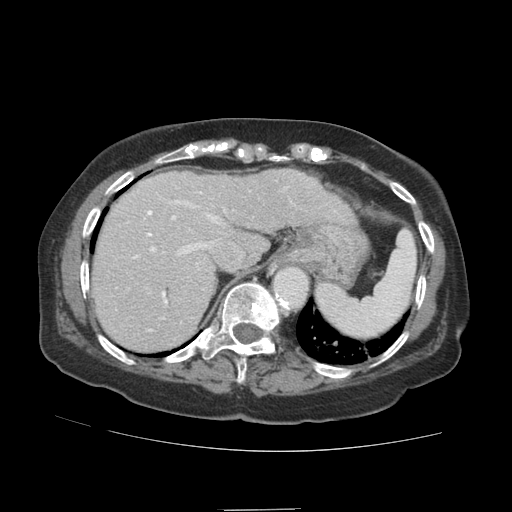
Contrast-enhanced abdominal CT (liver protocol), one axial slice. Slice 70 of 89 in the series (ordered by position). Reconstruction kernel STANDARD. Soft-tissue window (W 400 / L 40 HU). 512 × 512 image matrix, field of view 360 × 360 mm. From the clinical record (not read from this slice): diagnosis: hepatocellular carcinoma (patient treated with transarterial chemoembolisation; whether this scan precedes or follows treatment is not stated here); TNM stage (as recorded): Stage-II.
Structures marked on this image (semi-automatic segmentation, software-assisted and operator-edited):
- abdominal aorta: bounding box <274,267,307,305> (left, top, right, bottom; pixels)
- liver parenchyma outside the tumour (the mass and vessels are separate outlines, so this box may not span the whole liver): <92,168,330,350>
- liver vessels: <127,186,288,332>